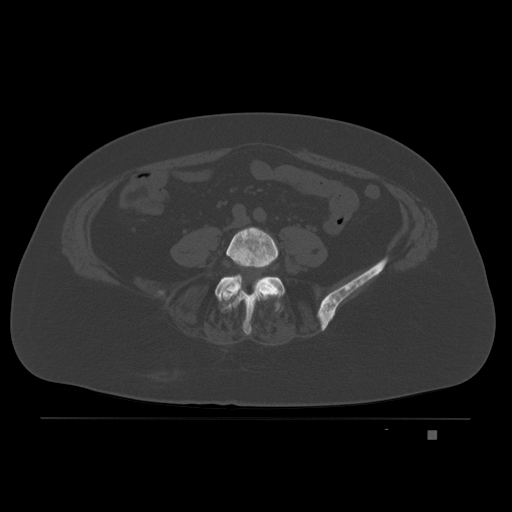
CT including the spine, one axial slice. Position 36 of 221 along the scan axis. Bone window (W 1800 / L 400 HU). 512 × 512 image matrix. Female patient, age 63 years. Case-level facts recorded for this patient, not image findings: primary cancer: breast.
Structures marked on this image (semi-automatically segmented with operator editing):
- L4 vertebra: bounding box [x1, y1, x2, y2] px = [215, 226, 278, 303]
- L5 vertebra: [215, 274, 286, 334]